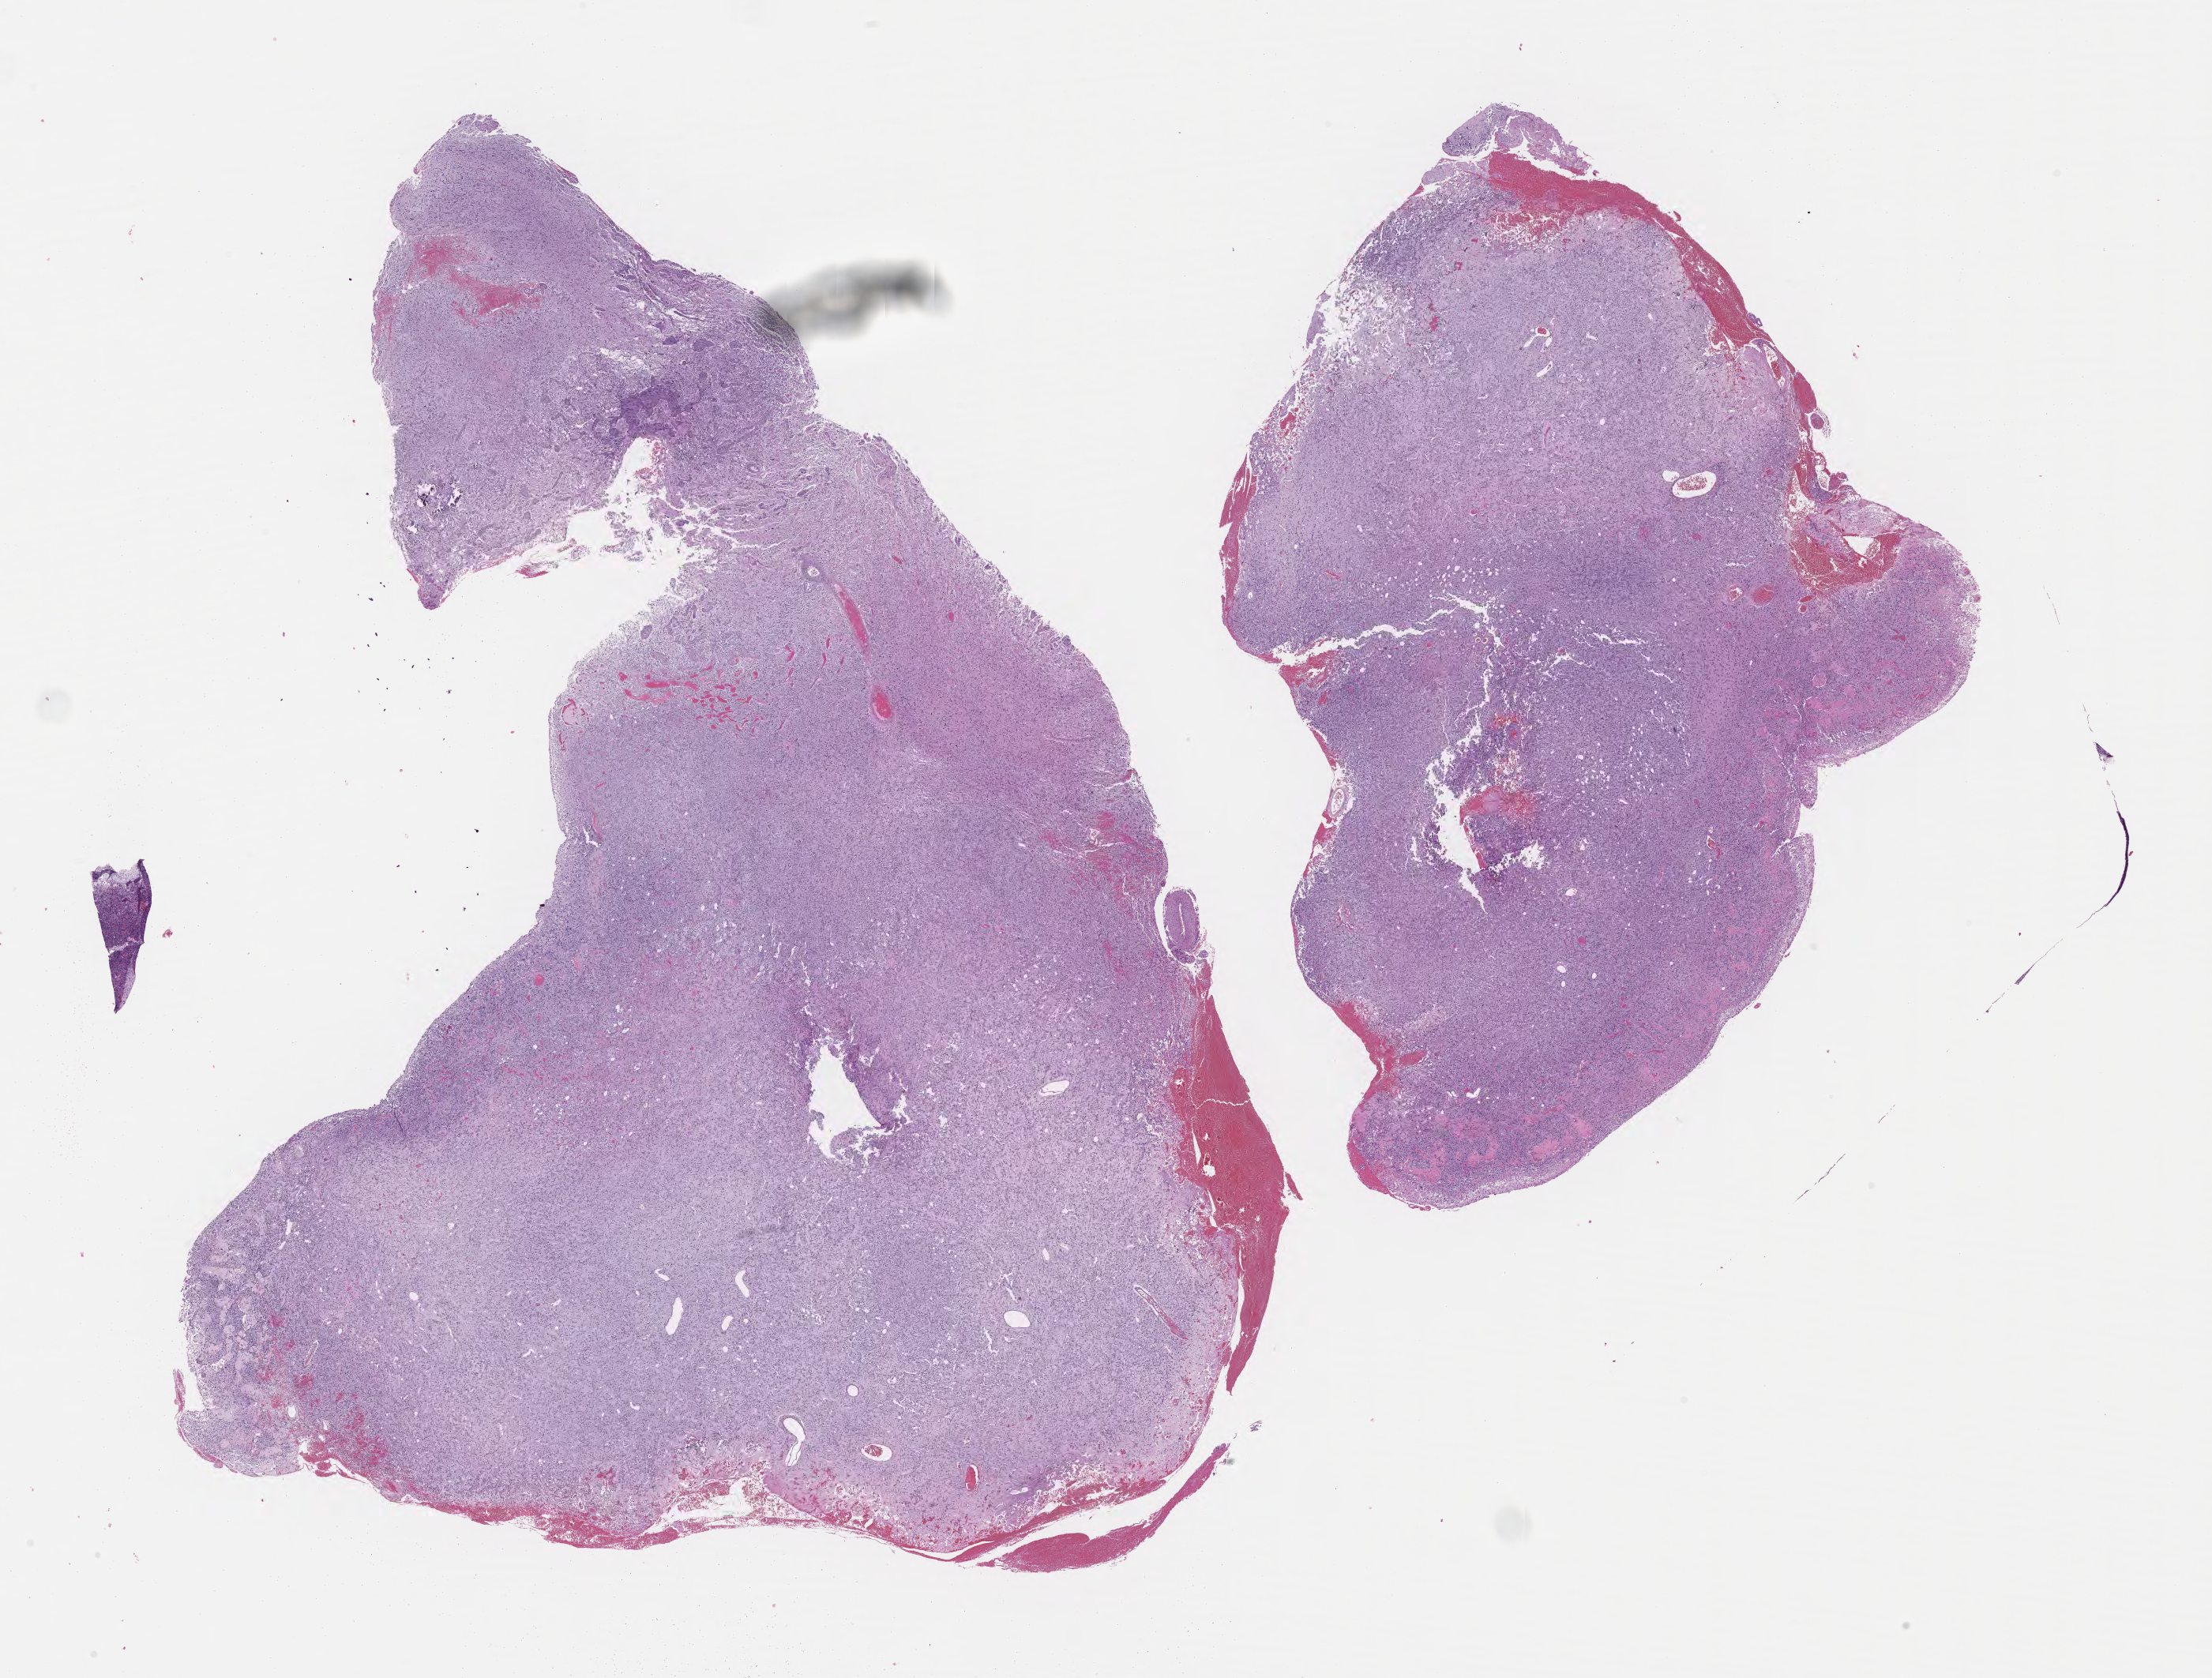
Haematoxylin and eosin whole-slide image of tumor tissue from the brain, shown as a low-resolution overview of the whole scanned area (about 22.6 x 17.2 mm); formalin-fixed, paraffin-embedded (FFPE) tissue. Patient male; age 45 months (3 years 9 months).
* diagnosis (ICD-O-3 morphology term): Ependymoma, NOS